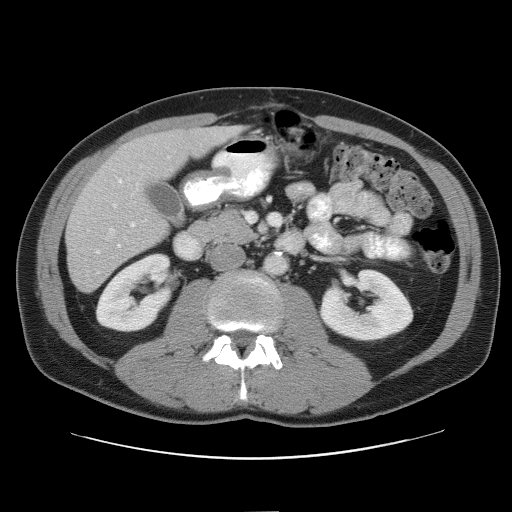
Contrast-enhanced abdominal CT, one axial slice. Slice 24 of 52 in the series (ordered by position). Reconstruction kernel STANDARD. 120 kVp. Intravenous contrast given. Soft-tissue window (W 400 / L 40 HU). 5 mm slice thickness. 512 × 512 image matrix, field of view 393 × 393 mm. Male patient, age 70 years. From the clinical record (not read from this slice): diagnosis: colorectal cancer liver metastases, imaged before liver resection; multiple liver metastases: yes; largest metastasis: 4 cm; chemotherapy before resection: yes.
Structures marked on this image (expert manual segmentation):
- hepatic veins: box from (x=84, y=176) to (x=132, y=254) px
- liver: (x=67, y=127)–(x=237, y=291)
- planned liver remnant (the part of the liver to remain after resection): (x=119, y=127)–(x=237, y=180)
- portal vein (with intrahepatic branches): (x=113, y=178)–(x=136, y=228)